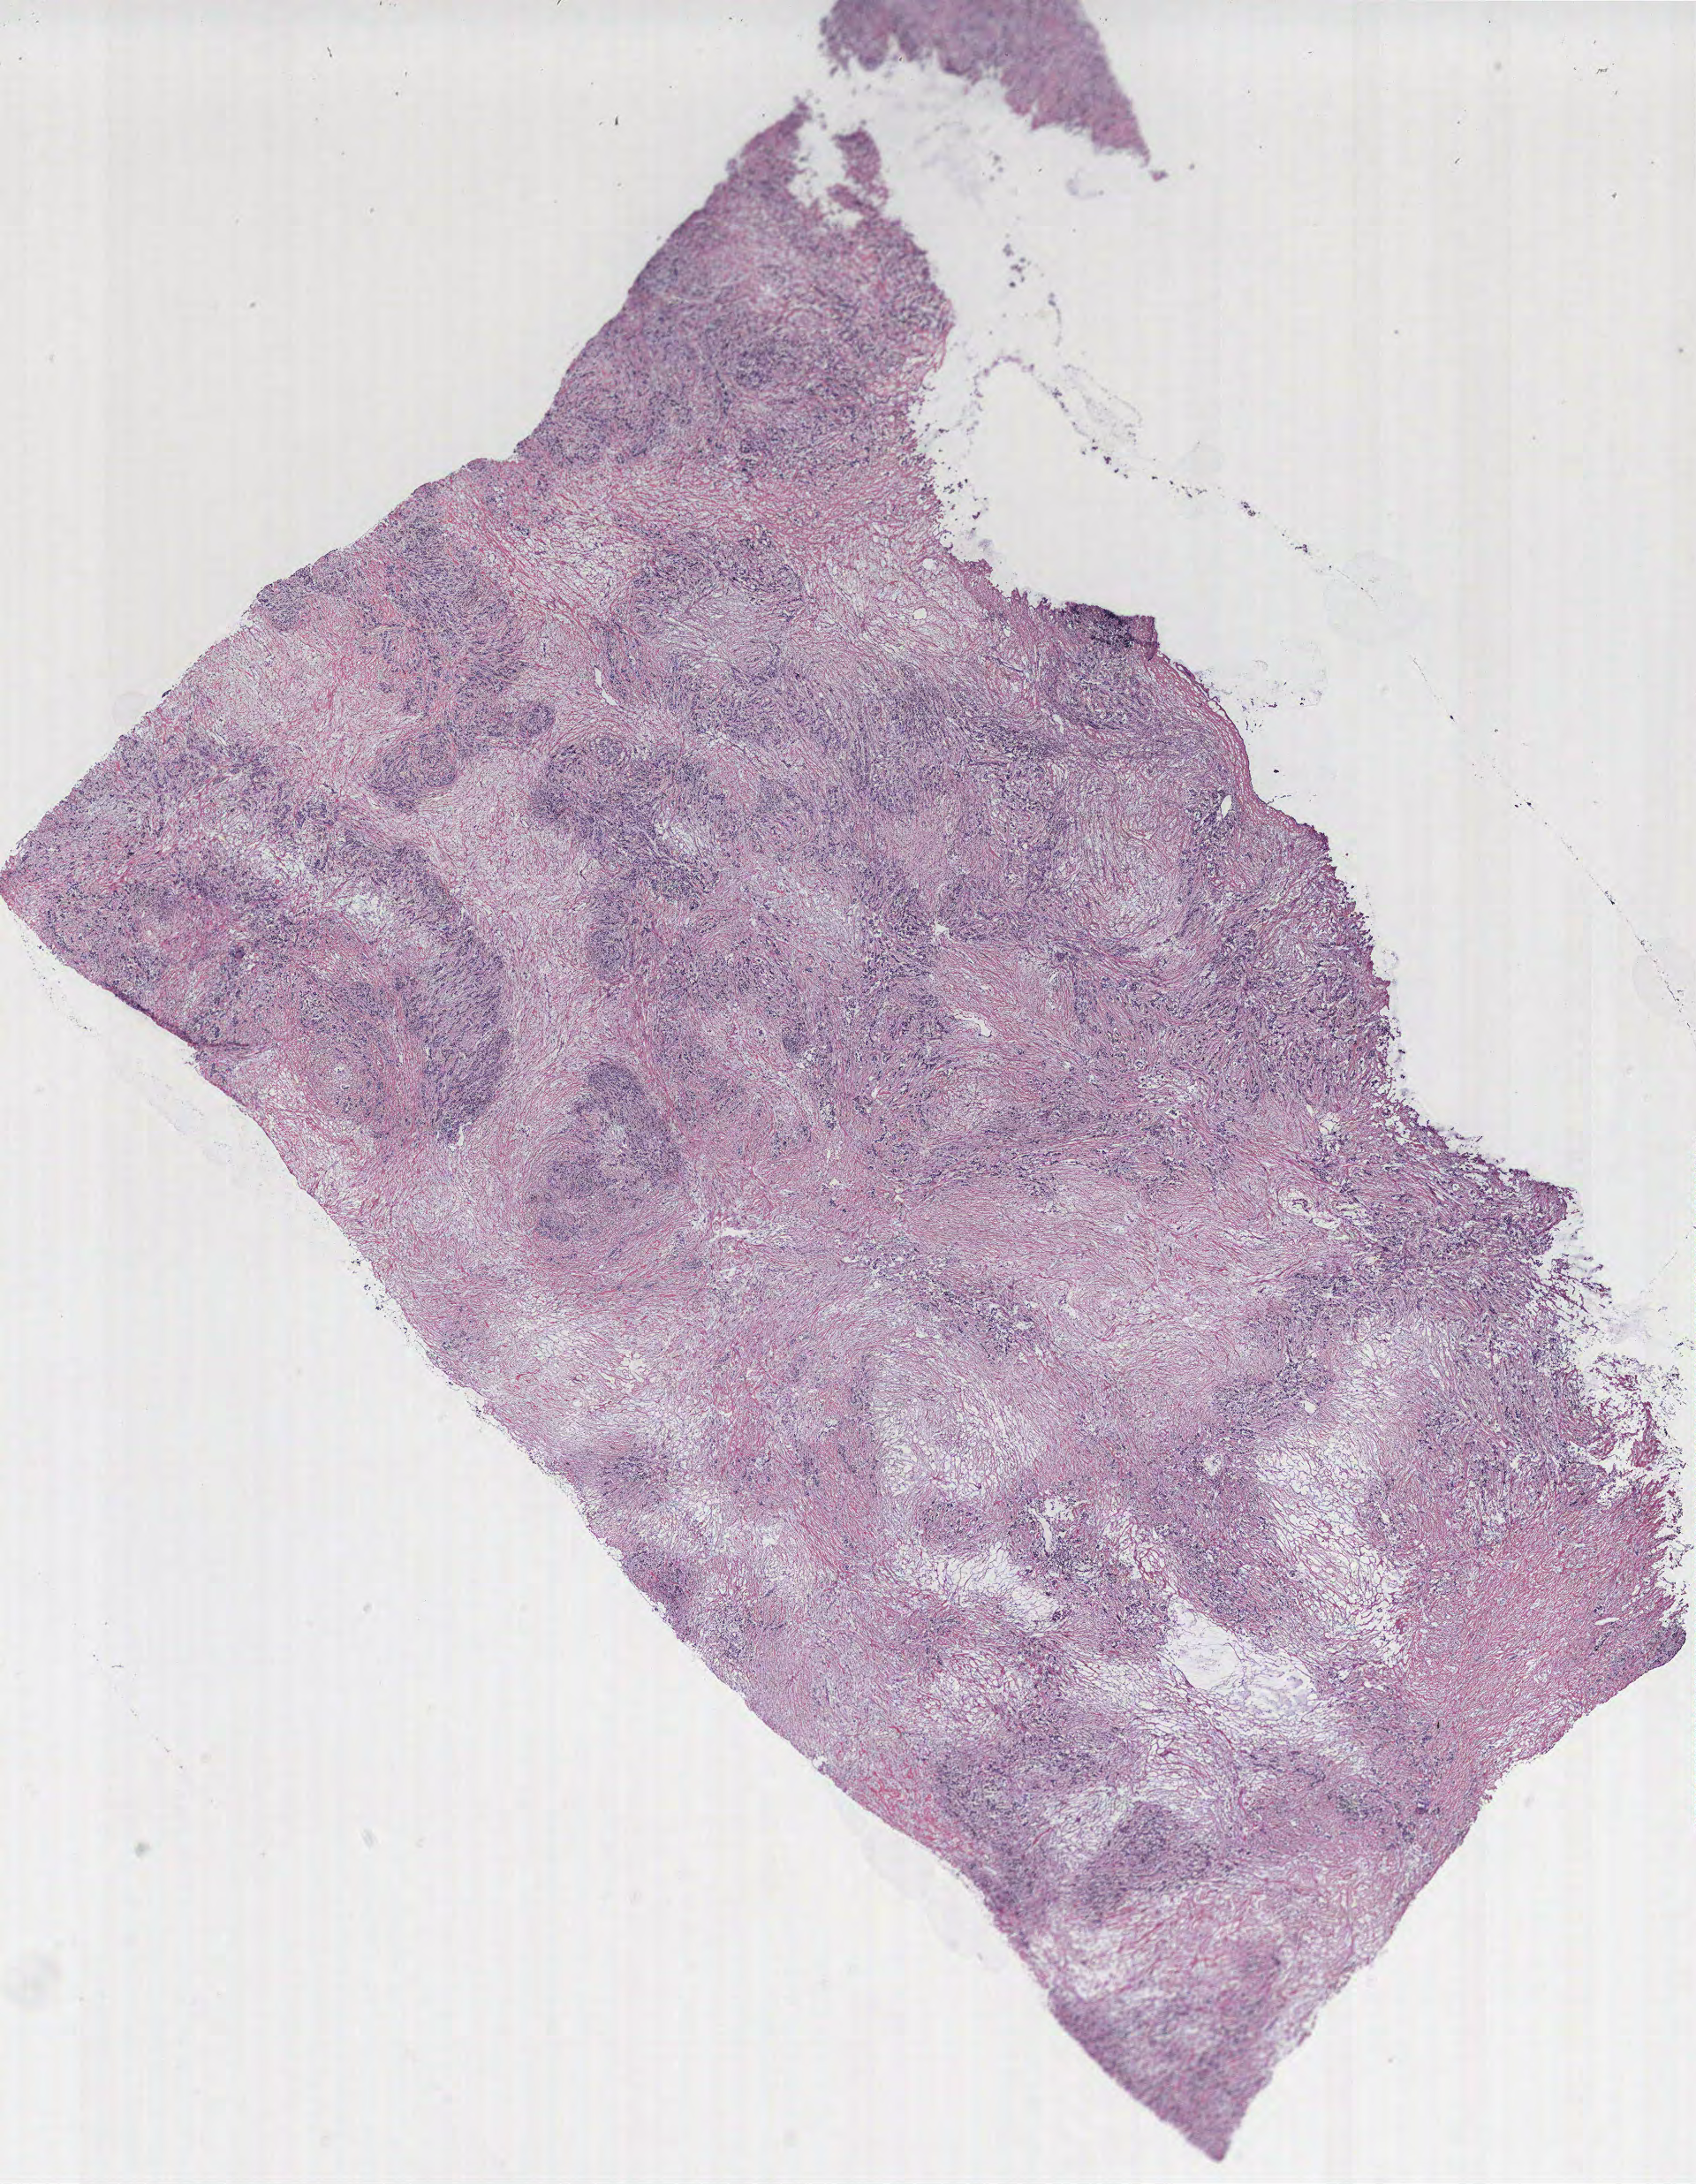
Digitized H&E-stained tissue section (whole slide) — shown as a low-resolution overview of the whole scanned area (about 15.4 x 19.8 mm), breast, tissue type not recorded. 64-year-old female patient.
Patient diagnosis: Infiltrating duct carcinoma, NOS.